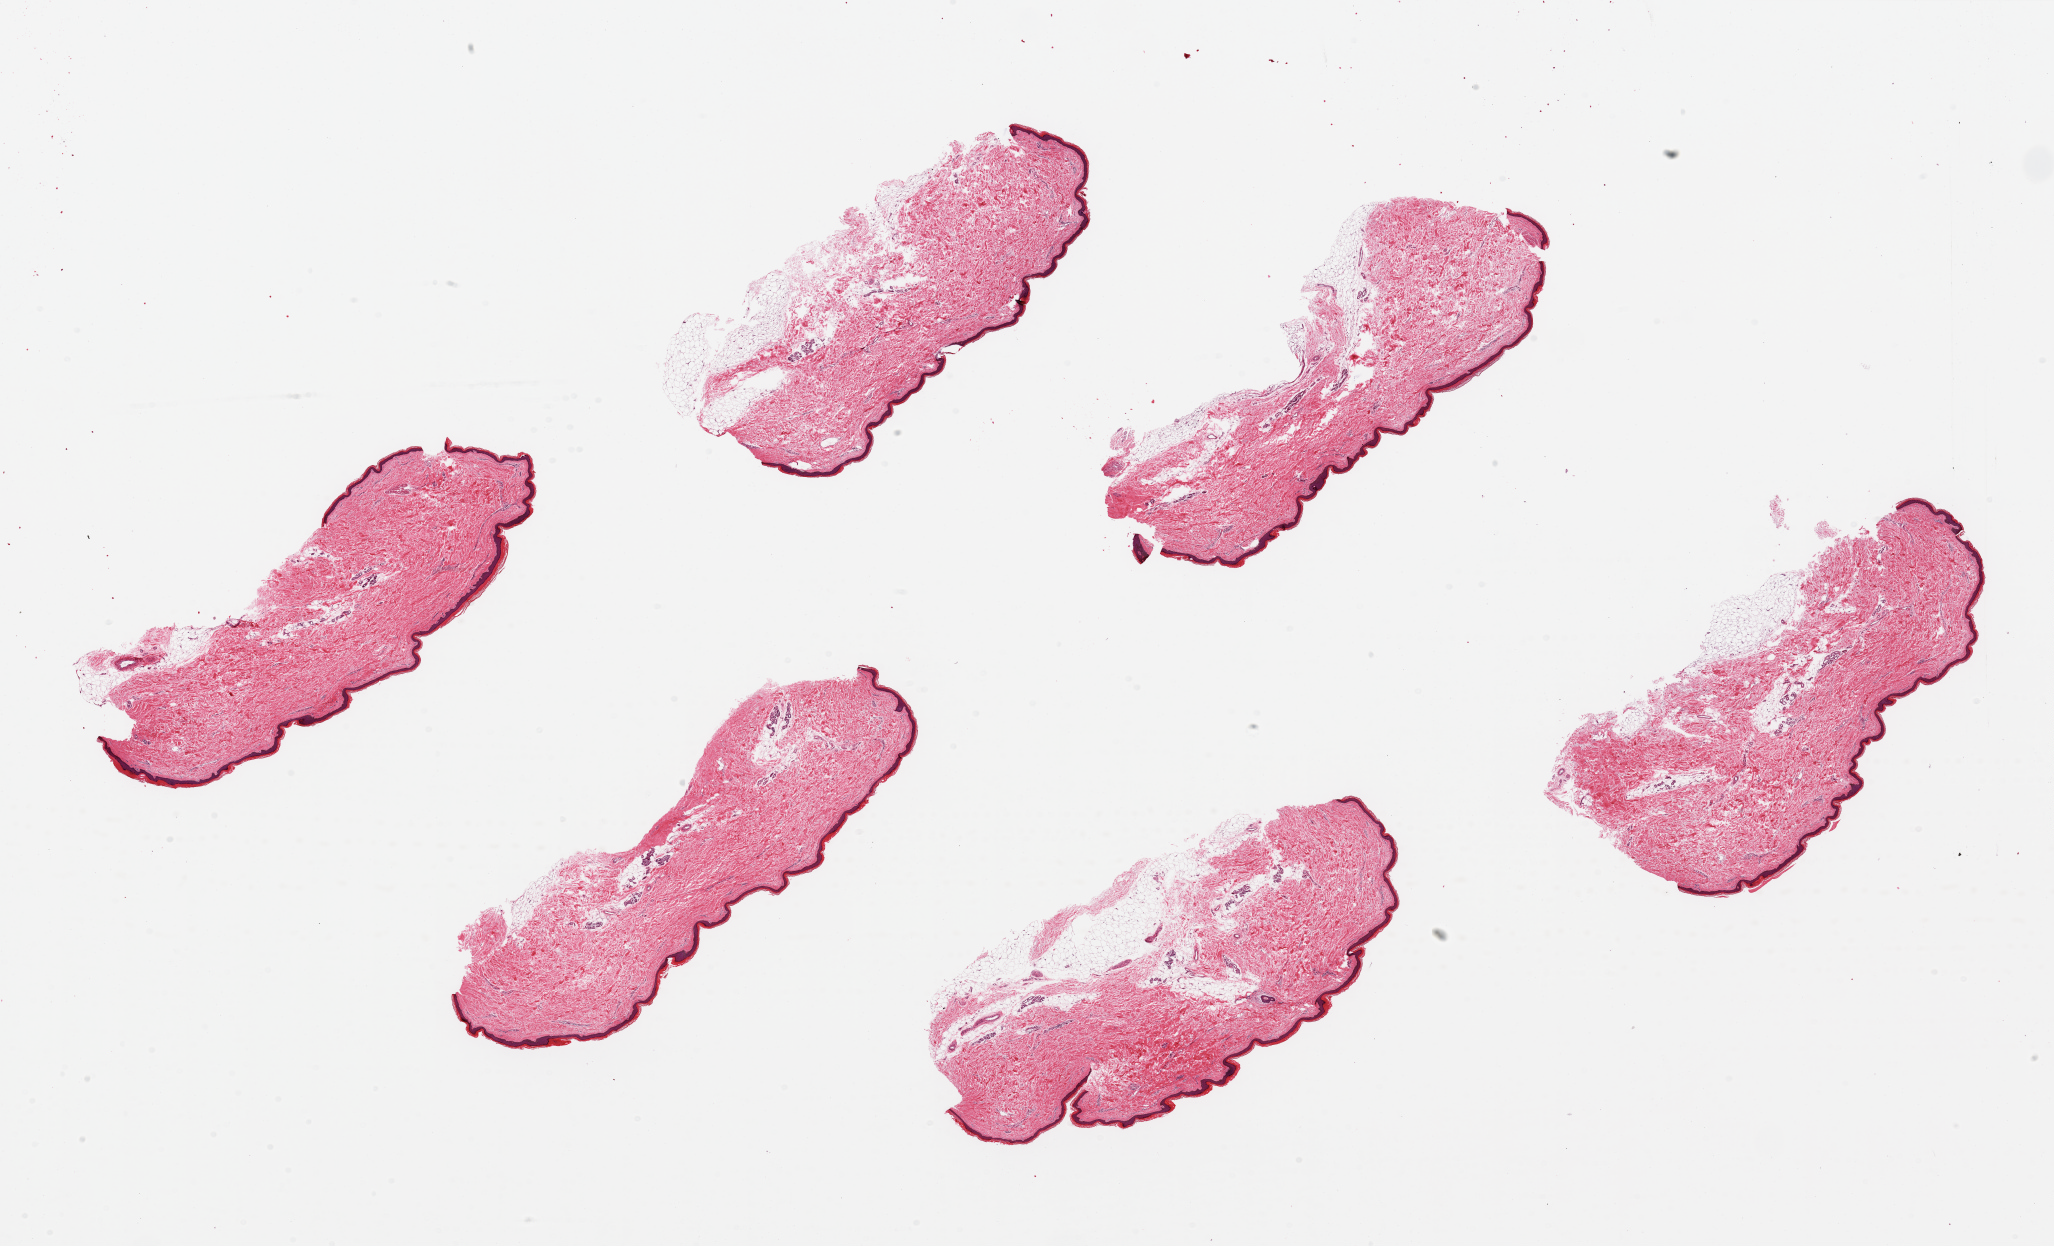
Whole-slide image, H&E stain, low-resolution overview of the scanned area, about 32.5 x 19.7 mm; PAXgene-fixed paraffin-embedded (PFPE) section; sampled site (target tissue): skin of lower leg; donor tissue sample. Female donor.
- reviewer comment on this tissue sample: 6 pieces, ~ 7.5x2.5mm. Squamous epithelium is 2-3% of thickness